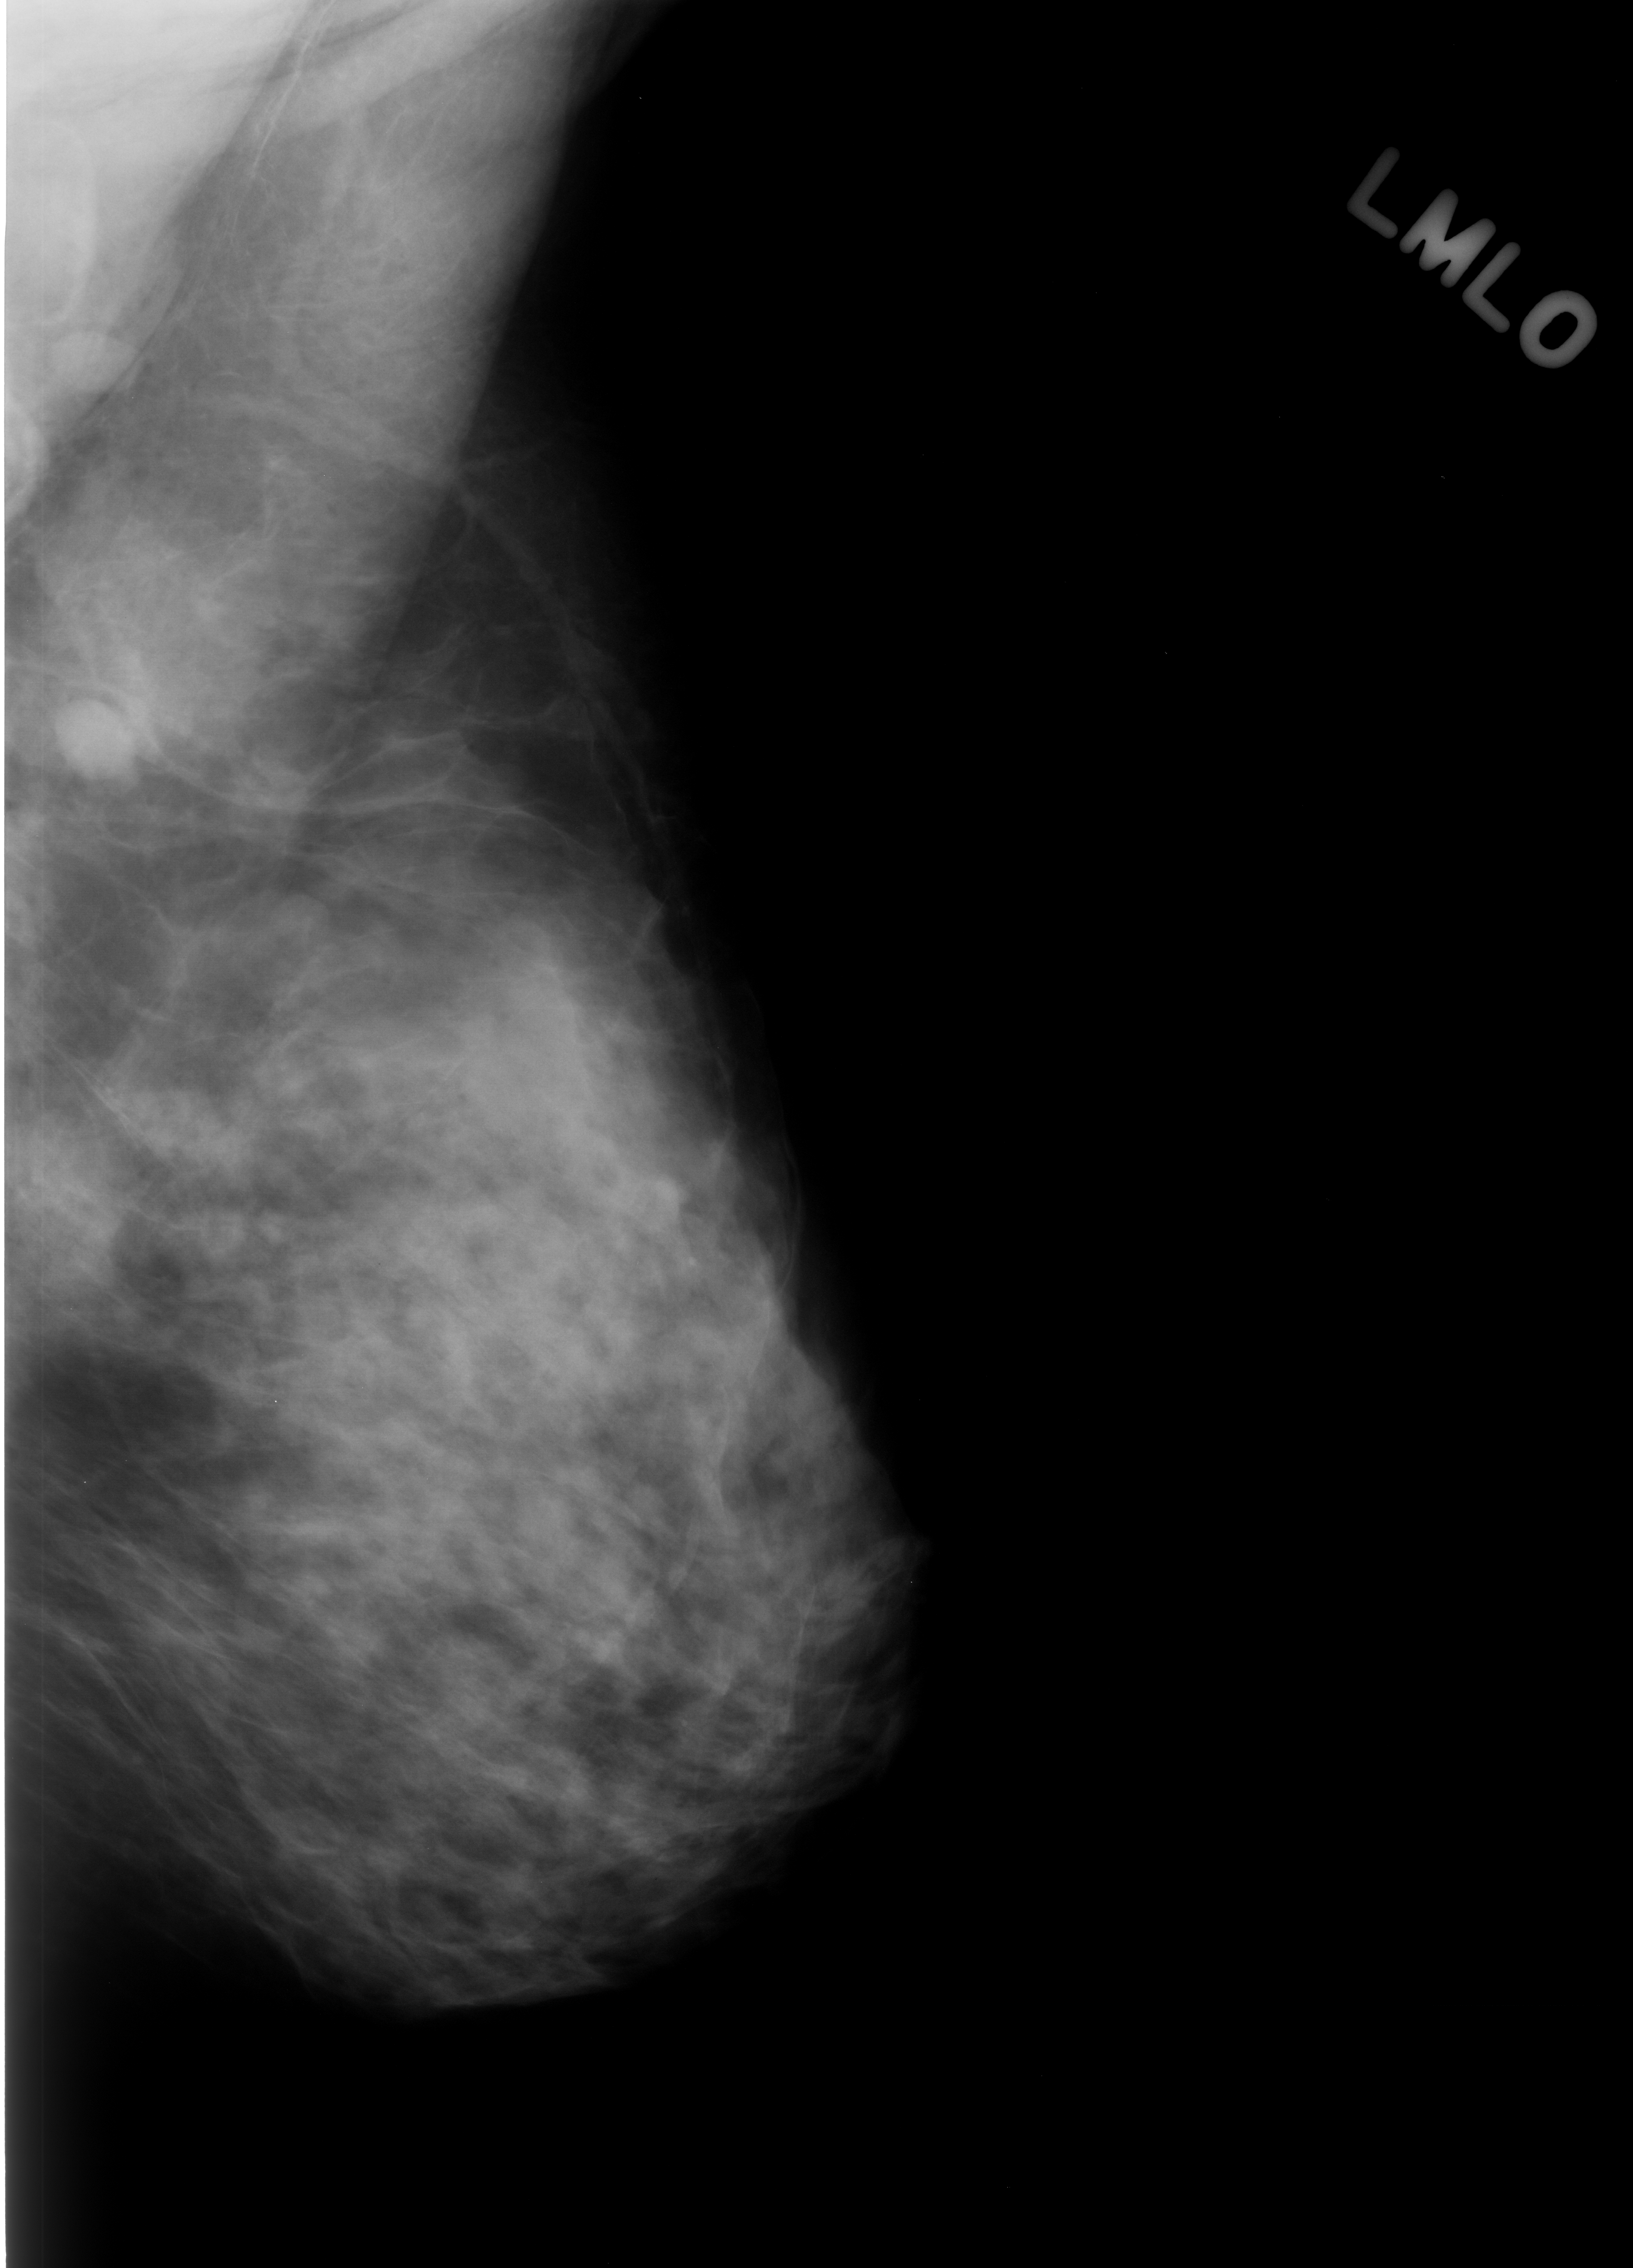
Digitized screen-film mammogram; left breast; MLO view; BI-RADS breast density category 3 (scale 1–4); 1633 × 2268 image matrix.
Expert-marked regions of interest on this film, with their recorded descriptors:
- Finding 1 of 2: mass, shape oval, margins circumscribed; BI-RADS assessment category 3; subtlety rating 5 on a 1 (subtle) to 5 (obvious) scale; pathology (as recorded): benign: bounding box (x1, y1, x2, y2) in pixels: (40, 305, 142, 410)
- Finding 2 of 2: mass, shape oval, margins circumscribed; BI-RADS assessment category 3; pathology (as recorded): benign: (47, 685, 165, 791)